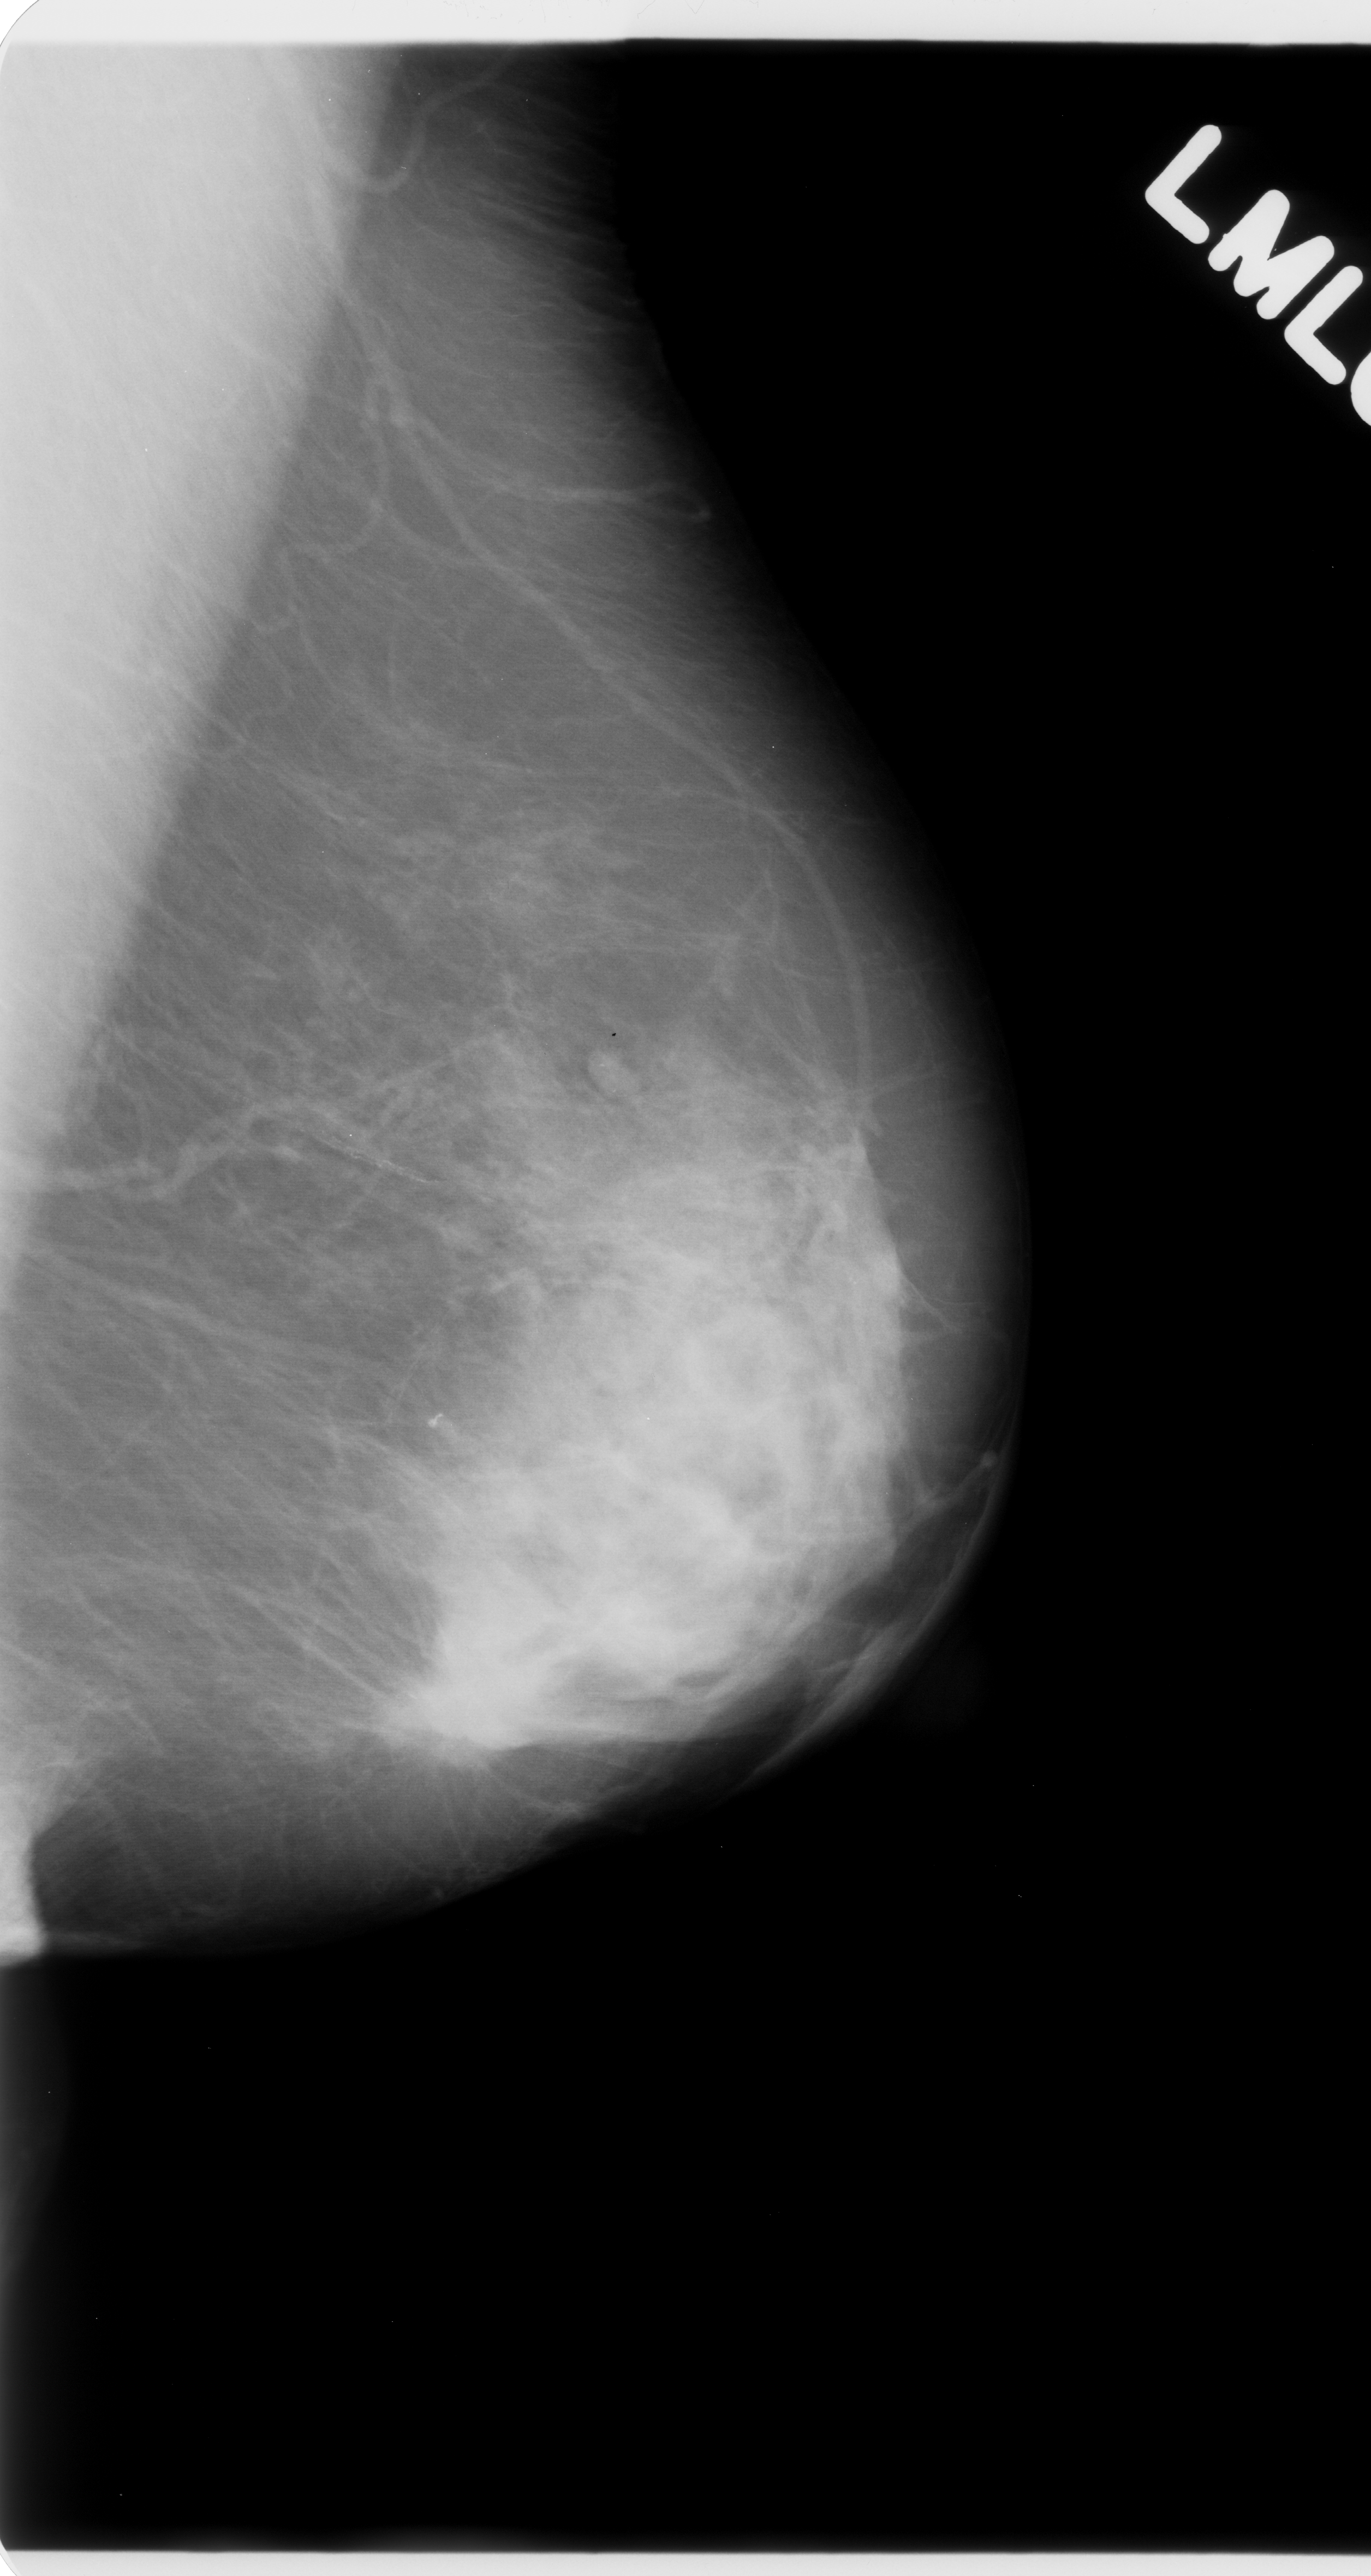
Mammogram (digitized film); left breast; MLO view; breast composition: heterogeneously dense (BI-RADS density category 3 of 4).
- Finding: mass, shape lobulated, margins spiculated; BI-RADS assessment category 5; subtlety rating 5 on a 1 (subtle) to 5 (obvious) scale; pathology result (as recorded, not read from the image): malignant.